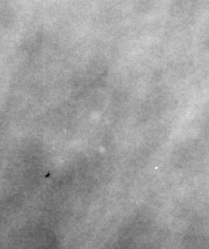
Cropped region of a digitized screen-film mammogram centred on a radiologist-marked abnormality, right breast, MLO view.
Calcifications, morphology amorphous / pleomorphic, distribution clustered; BI-RADS assessment category 4; pathology result (as recorded, not read from the image): benign.